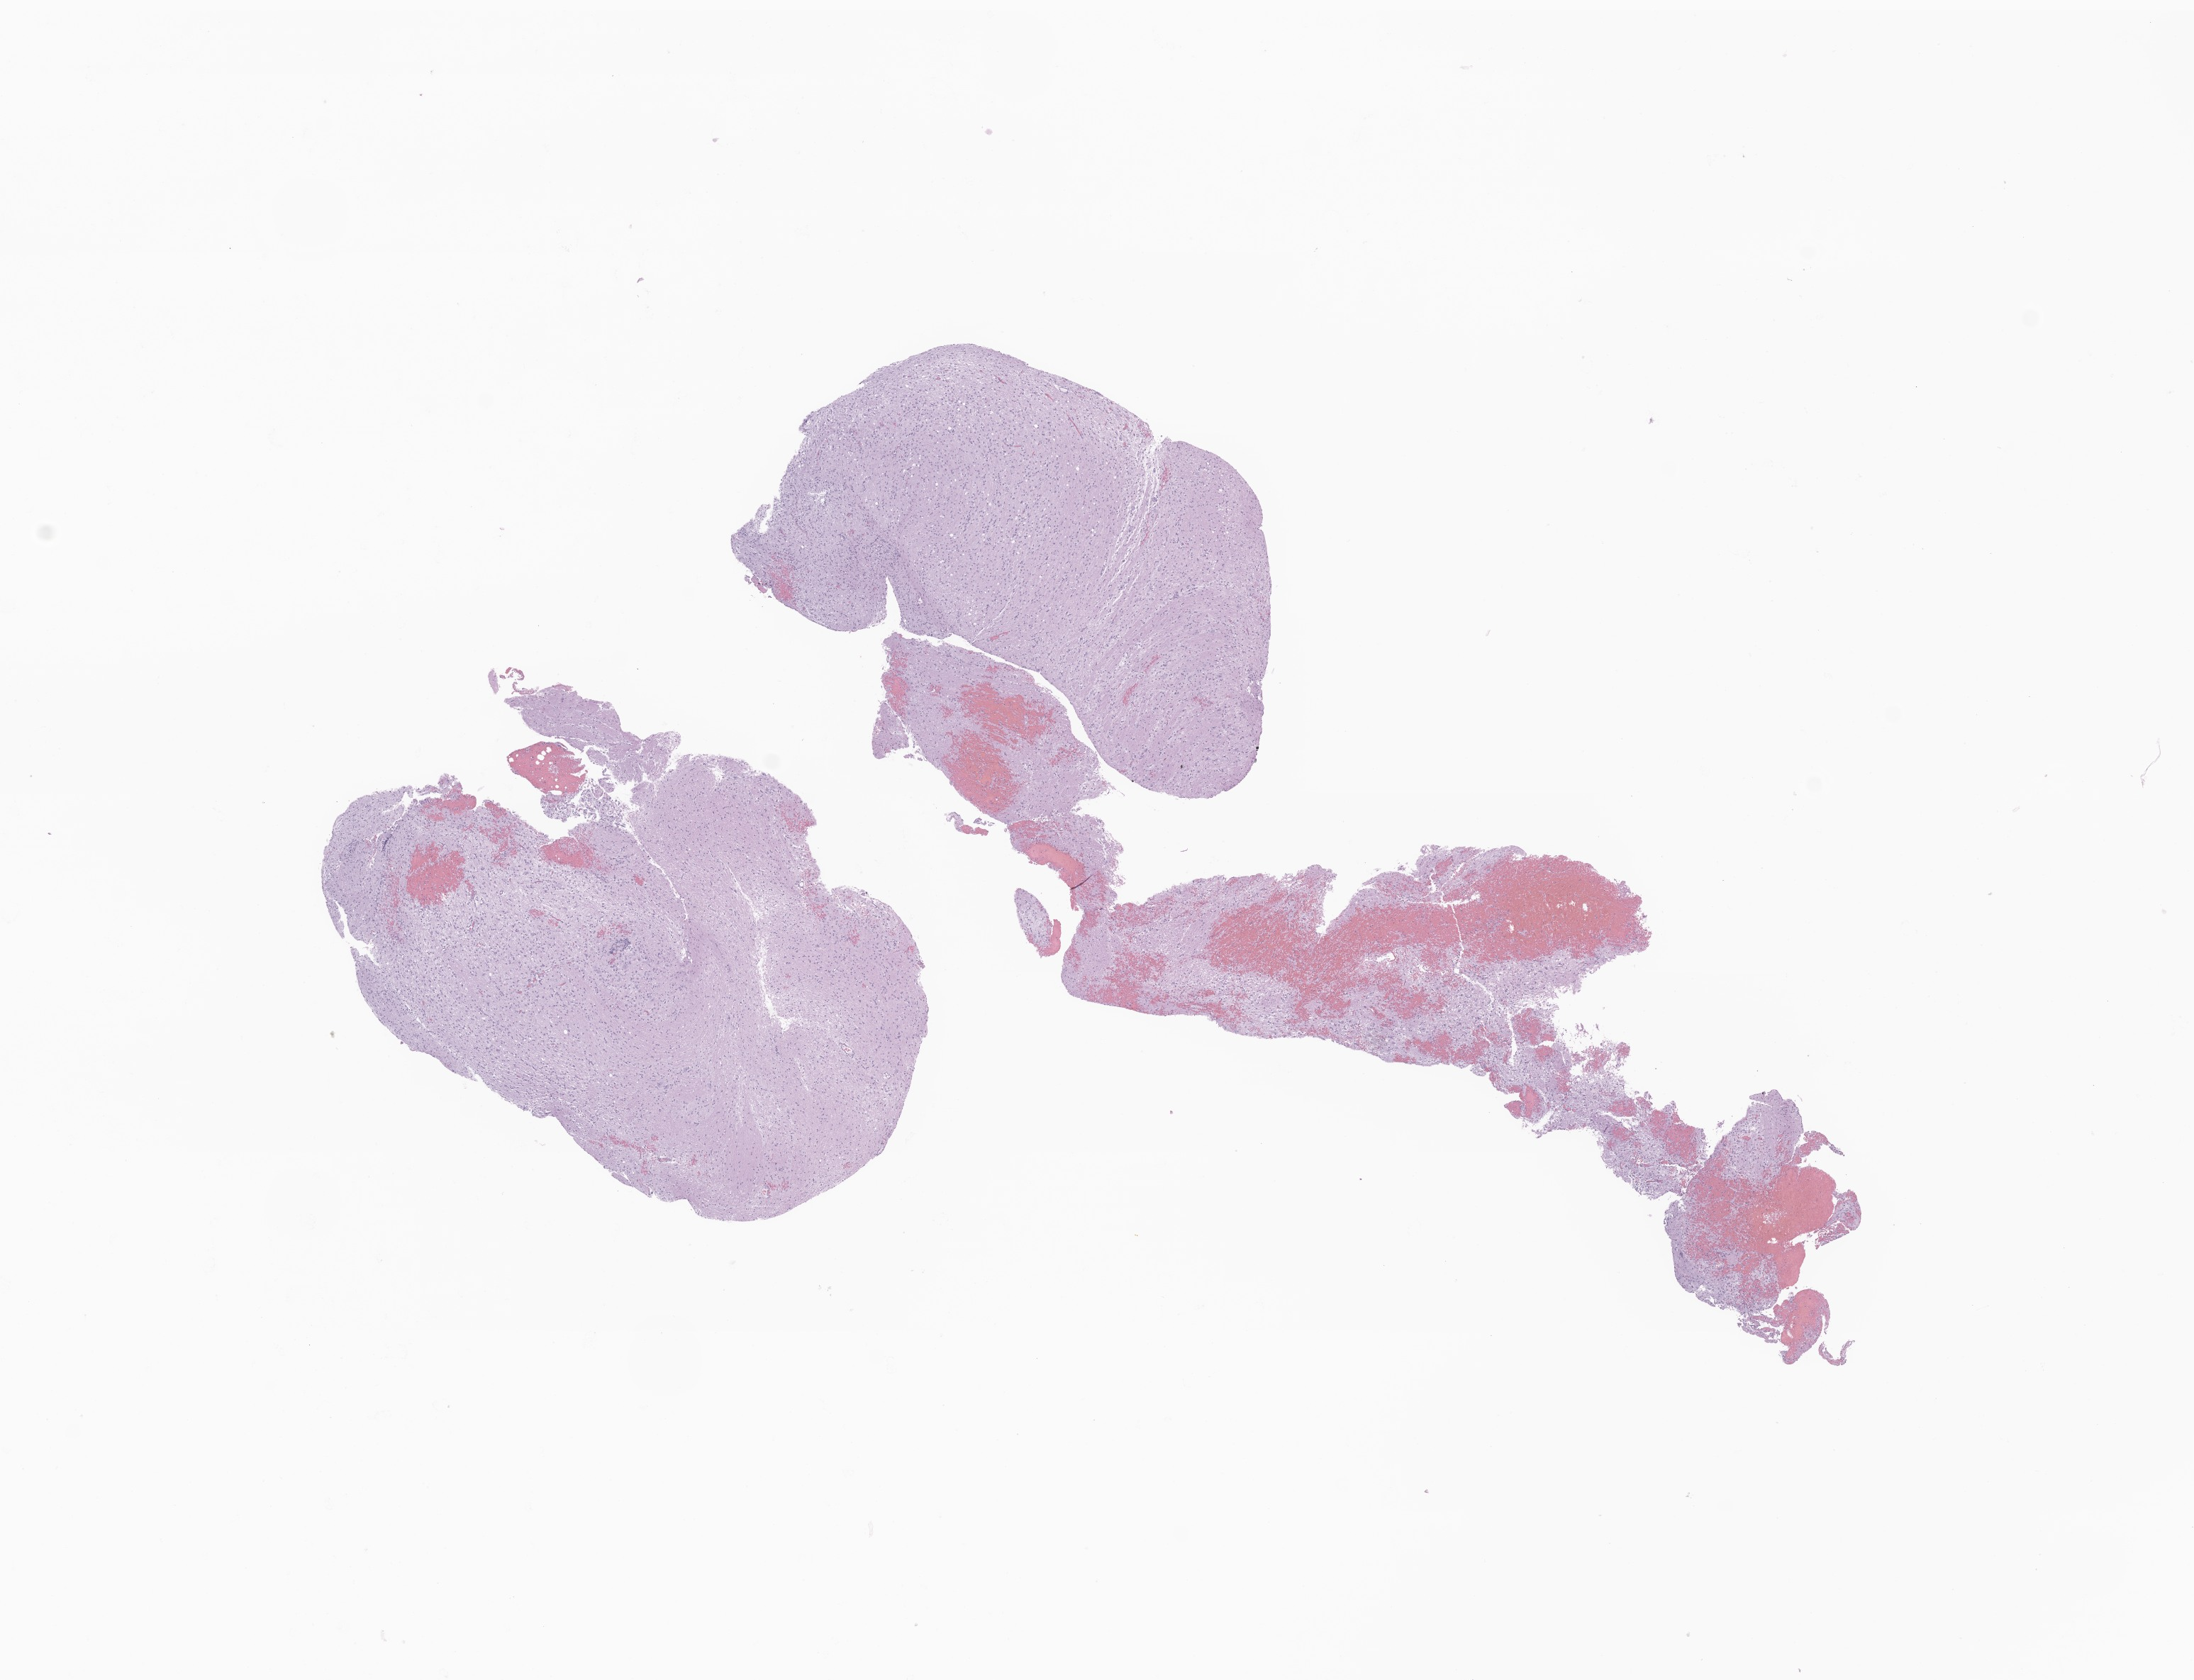
Whole-slide image, H&E stain of tumor tissue from the brain, low-resolution overview of the scanned area, about 13.0 x 10.0 mm, formalin-fixed paraffin-embedded section. Male patient, age 205 months (17 years 1 month).
Diagnosis: Glioma, malignant.